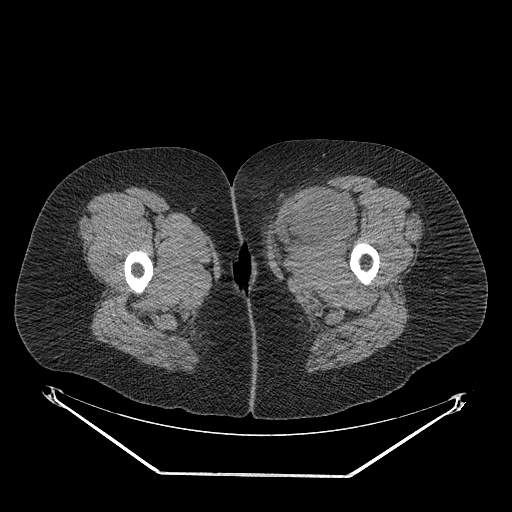
CT of an extremity soft-tissue mass (from a PET/CT study), one axial slice; position 35 of 267 along the scan axis; 140 kVp; soft-tissue window (W 400 / L 40 HU); 3.75 mm slice thickness; 512 × 512 image matrix, field of view 500 × 500 mm. Female patient. From the clinical record (not read from this slice): histological type: myxofibrosarcoma; grade: intermediate; site of the primary tumour: left thigh.
Annotated regions visible in this slice (expert contour drawn on MRI and transferred to this co-registered scan by the dataset authors):
- gross tumour volume including surrounding oedema: bounding box [x1, y1, x2, y2] px = [267, 187, 359, 259]
- gross tumour volume (mass): [270, 187, 353, 243]